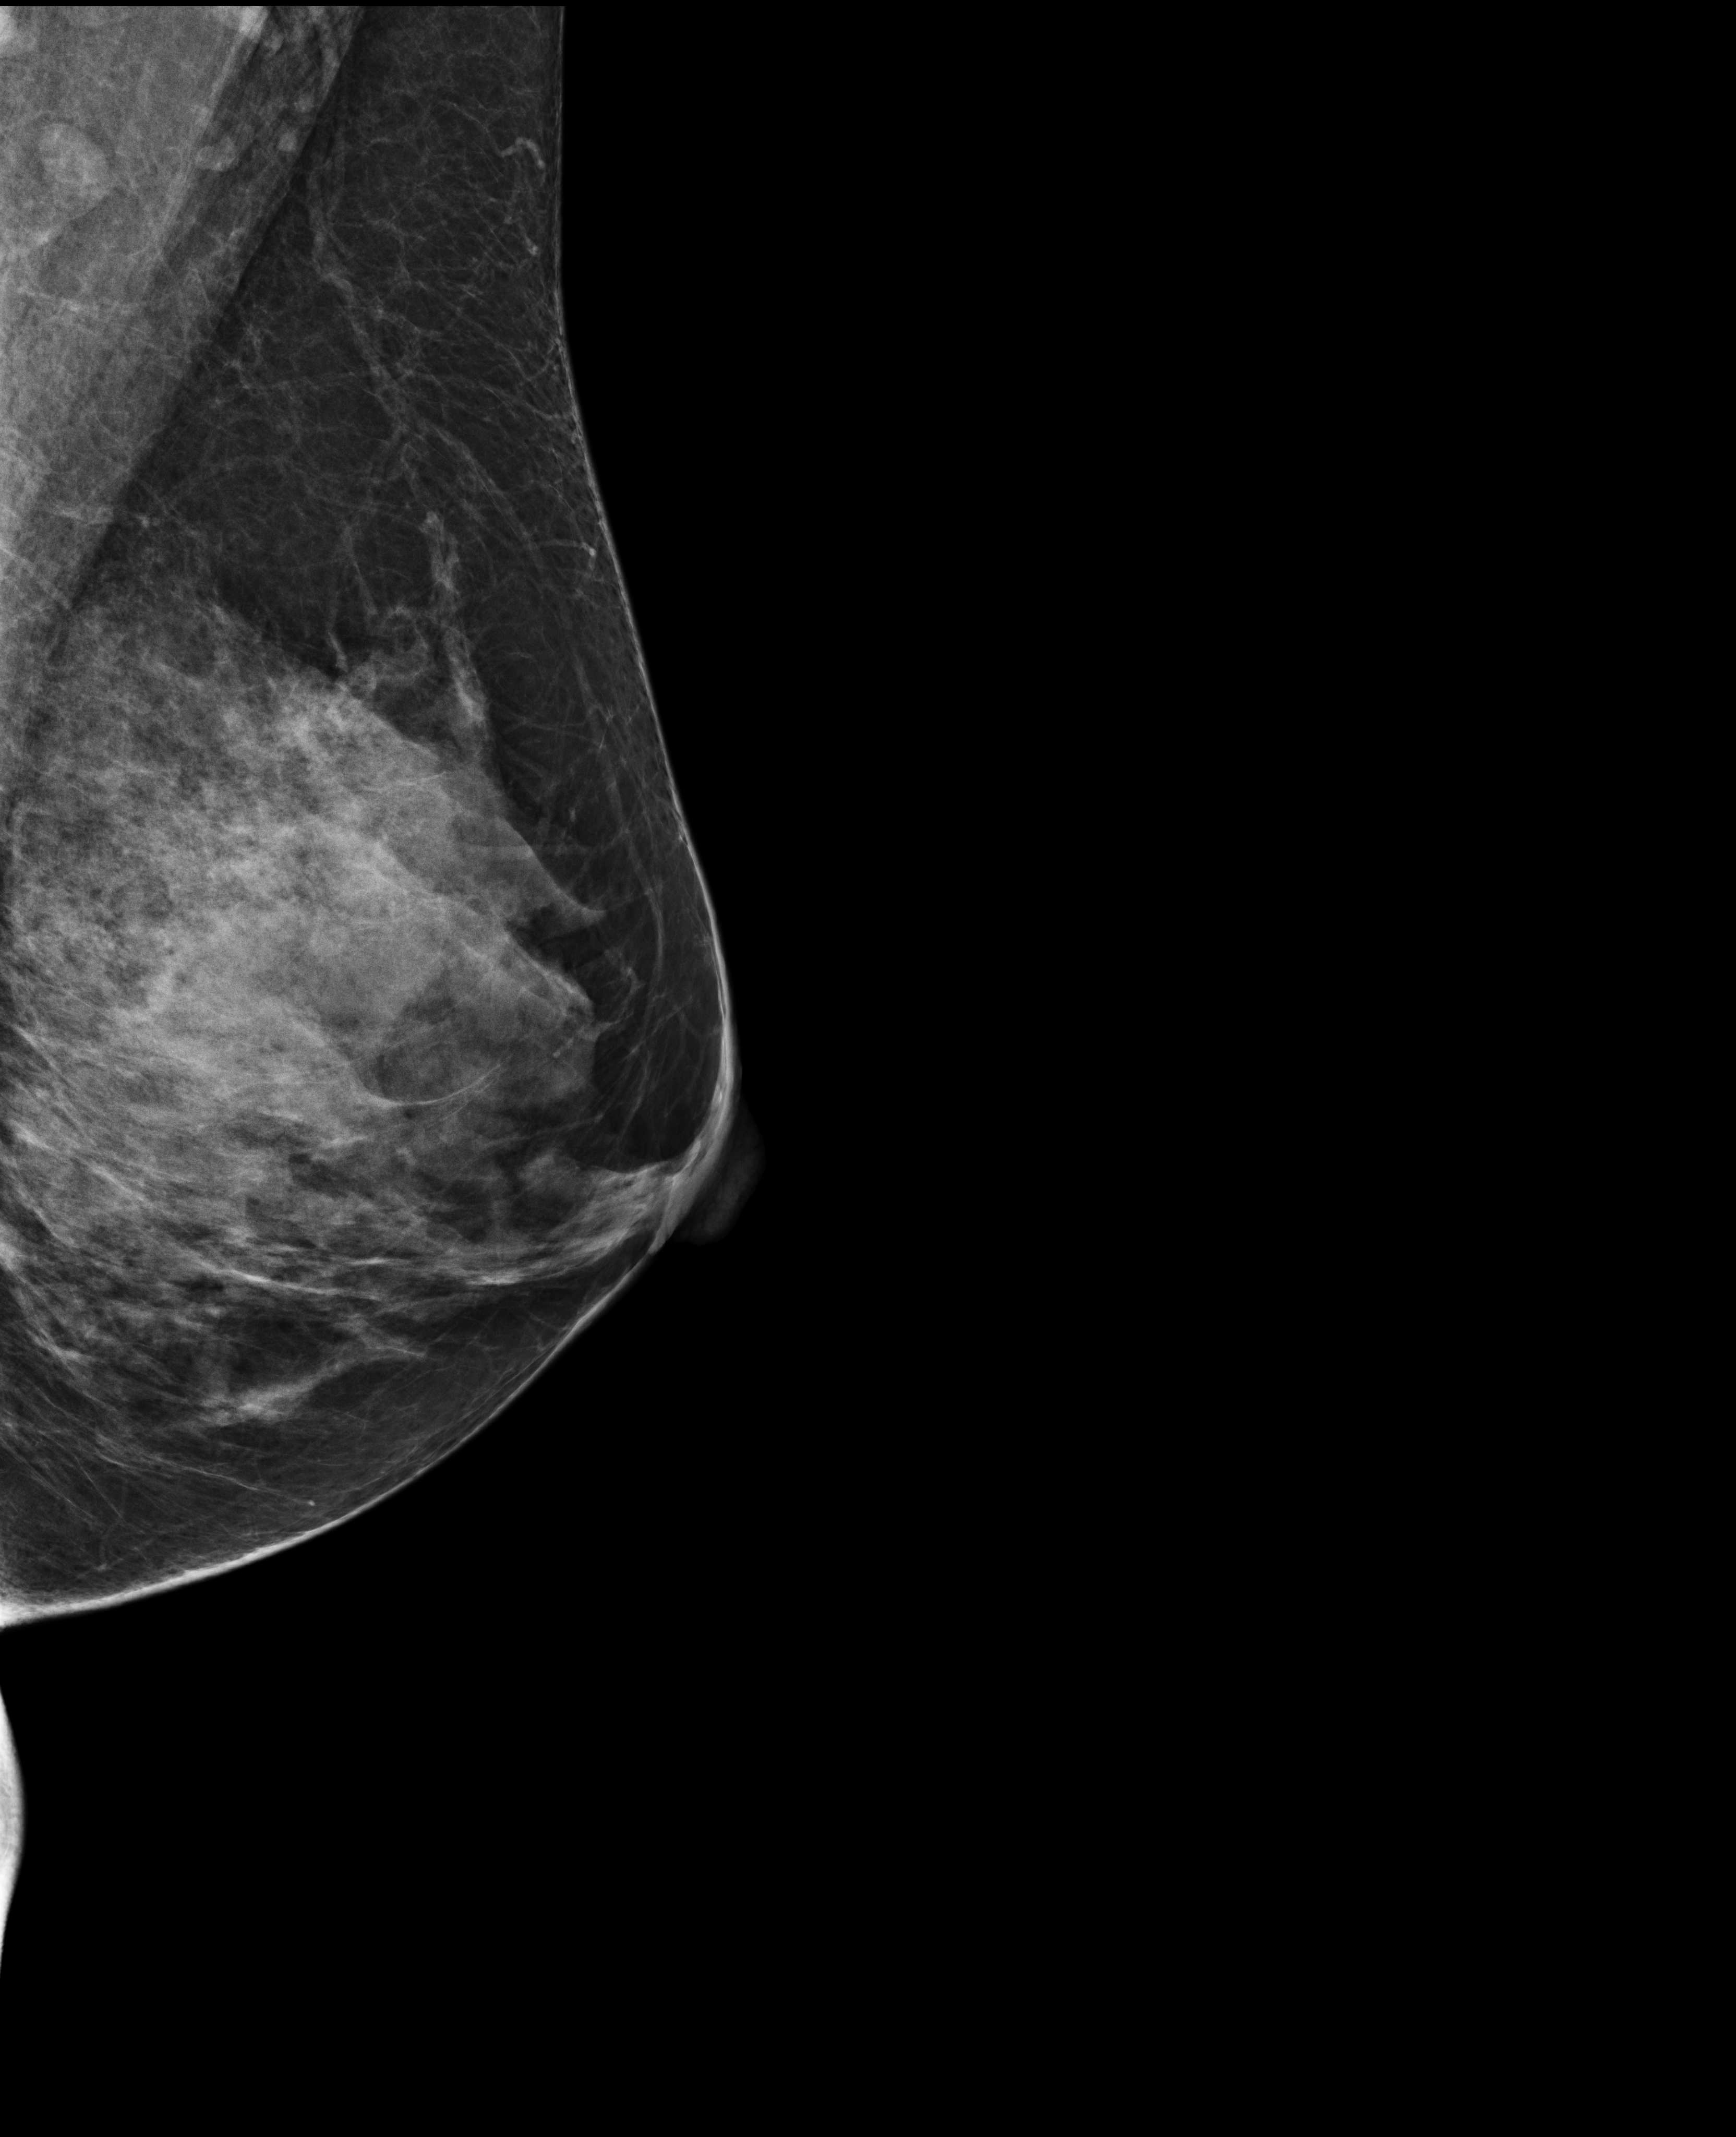
Annual screening mammography examination; system: Selenia Dimensions. Patient aged 50 years (female).
Image type: full-field digital mammogram. Breast: left. Projection: medio-lateral oblique projection. Breast density at the screening exam (both breasts): extremely dense (BI-RADS density category d). Final BI-RADS category for the screening round (tomosynthesis exam, both breasts): category 1. Recall: no recall after this screen.